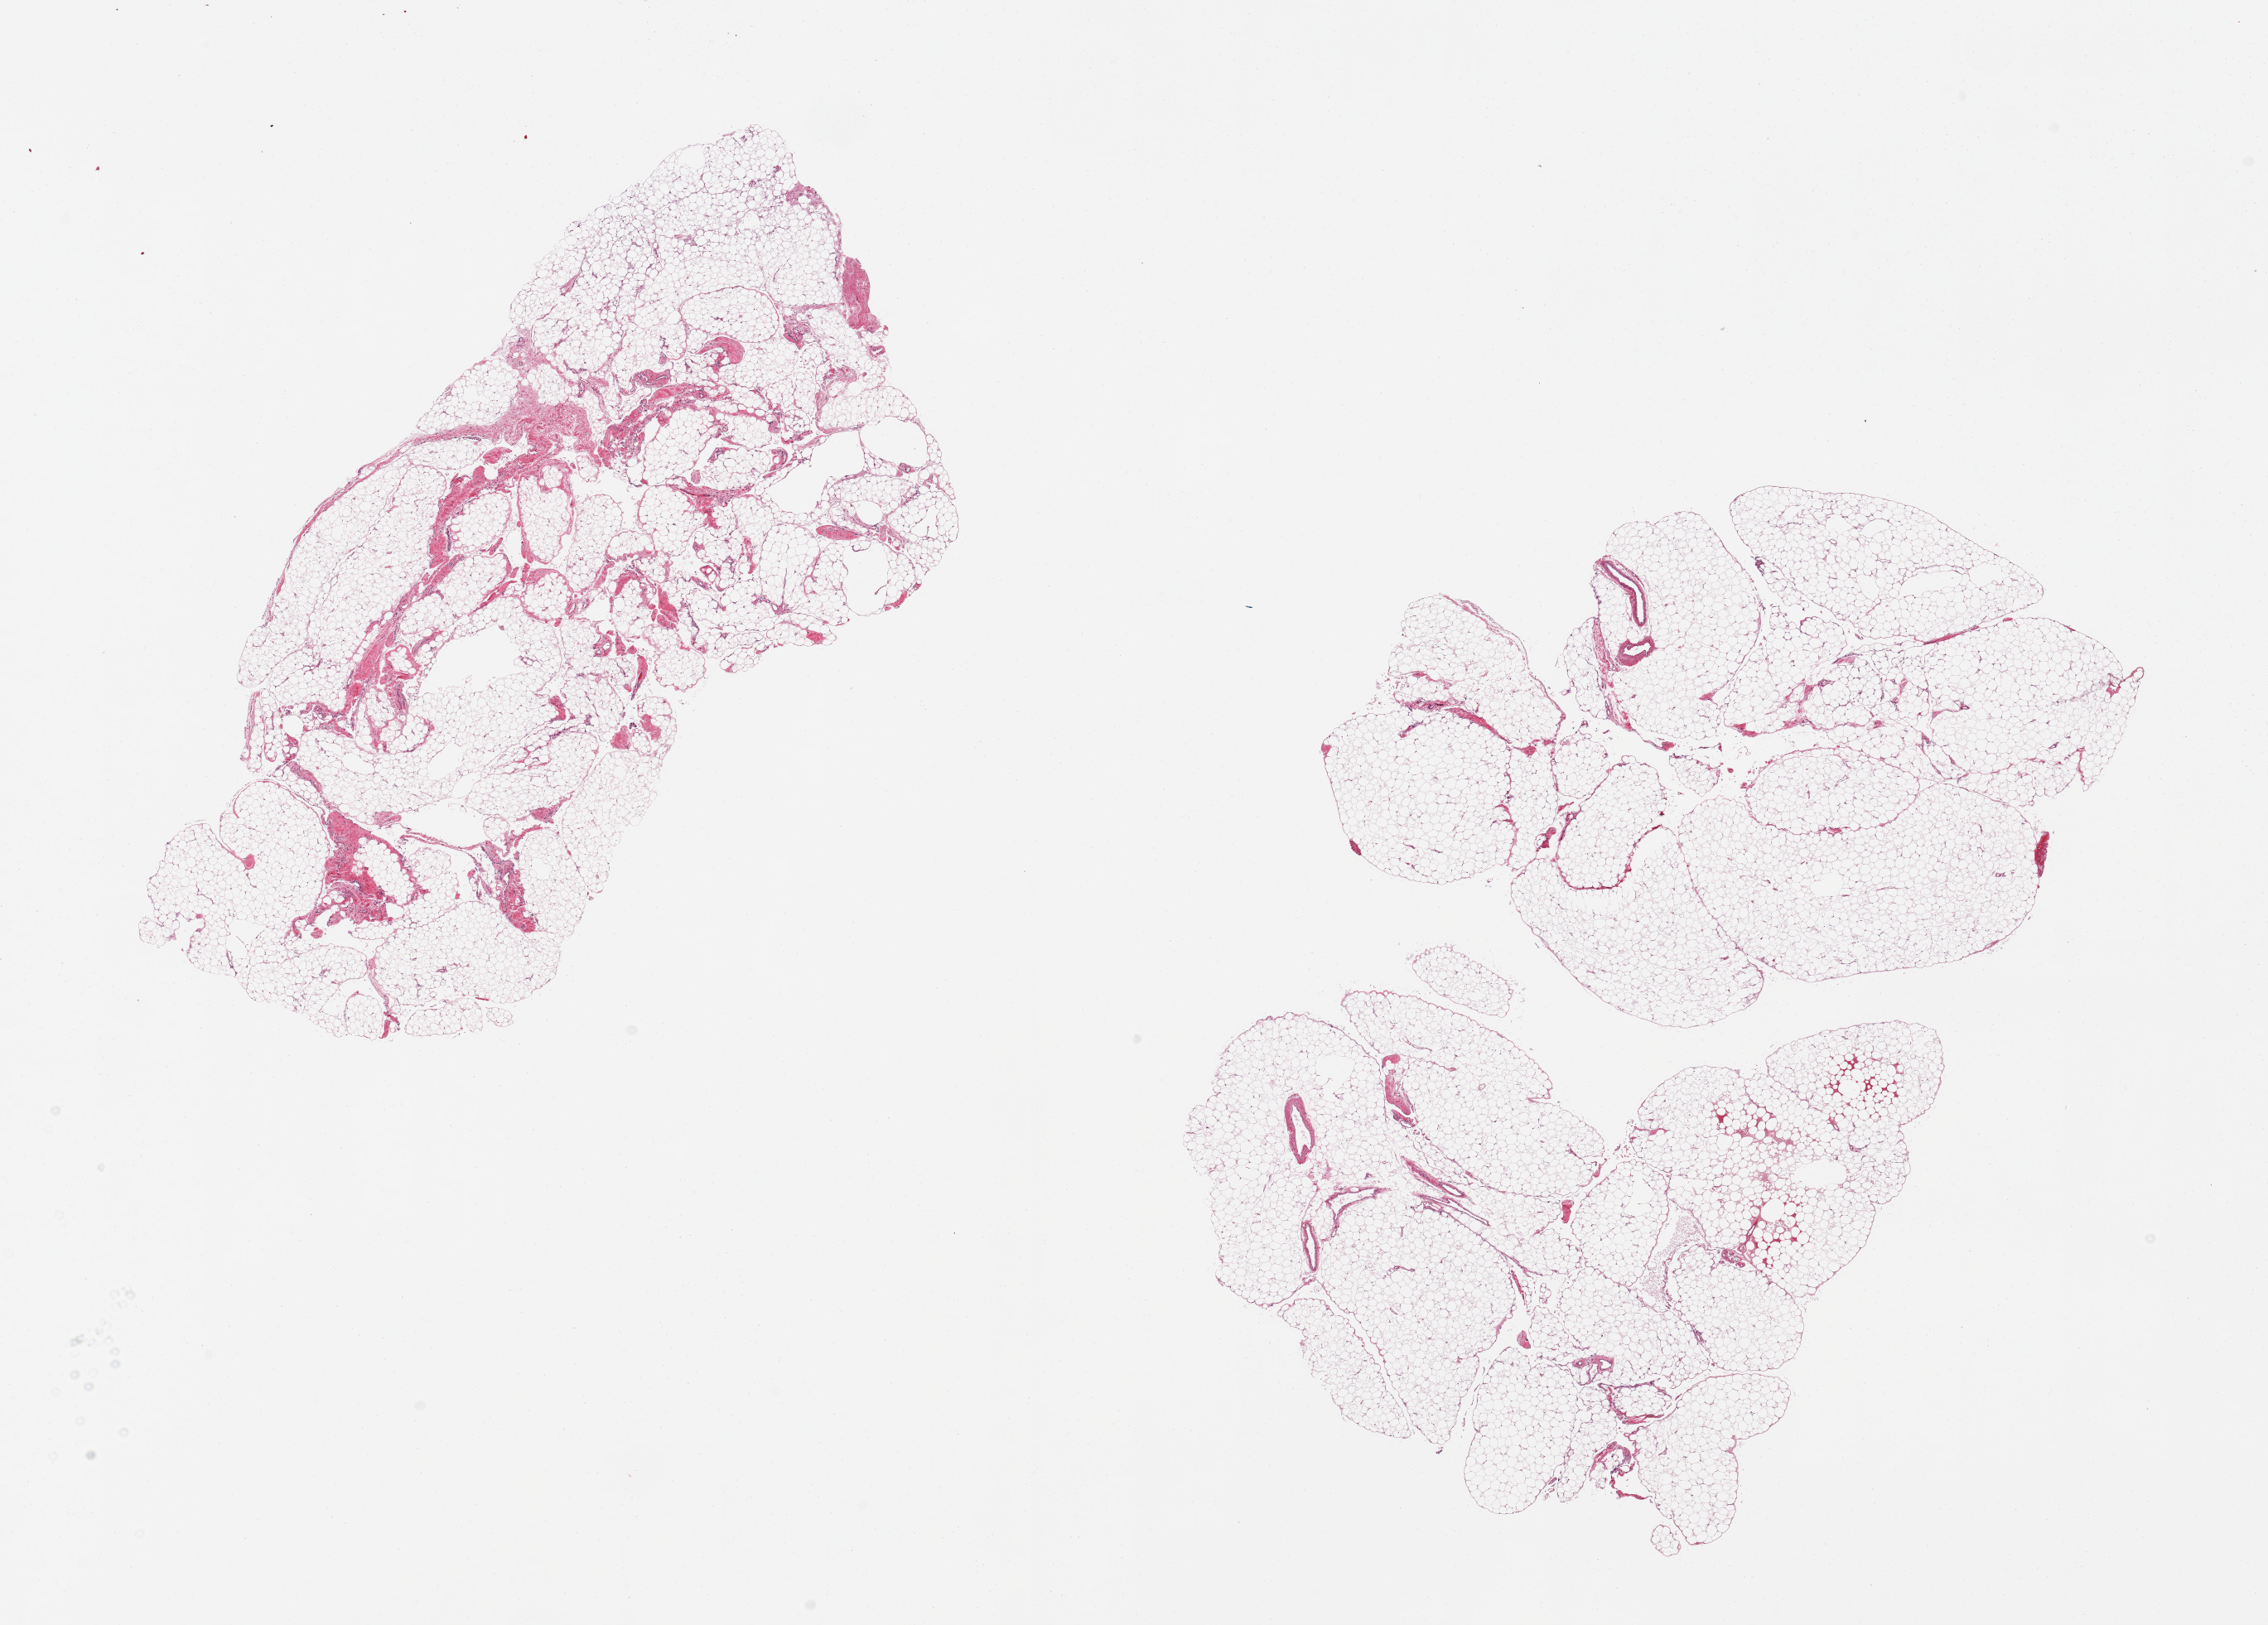
Whole-slide image, haematoxylin and eosin stain — shown as a low-resolution overview of the whole scanned area (about 21.7 x 15.5 mm, slide scanned at 20x); PAXgene-fixed paraffin-embedded (PFPE) section; section of omentum (target tissue); tissue donor sample. Male donor.
- pathologist's review note for this sample: 2 pieces, ~15% fascia/vascular elements